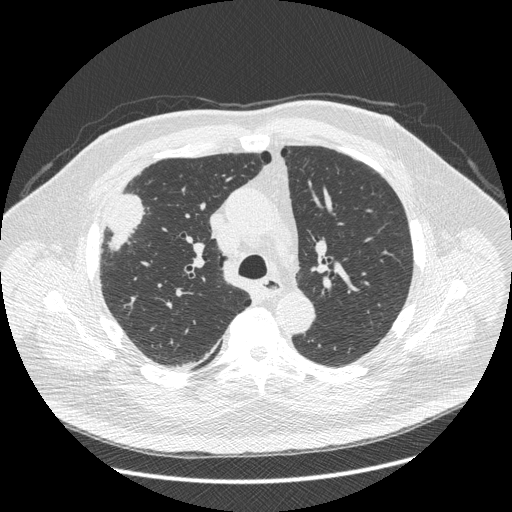
Axial slice from a low-dose chest CT screening exam; third annual screen; lung window (W 1500 / L -600 HU); 1.25 mm slice thickness; standard (soft-tissue) reconstruction kernel (STANDARD); slice 139 of 426 in the series. Male, age 66 years at enrolment. Current smoker at enrolment.
Expert reader's lesion annotation, bounding box (x1, y1, x2, y2) in pixels: (87, 190, 146, 266). Screening reader's record for this exam (one nodule recorded; not confirmed to be the boxed lesion): non-calcified nodule or mass ≥4 mm, right upper lobe, 48 × 25 mm, spiculated (stellate) margins, soft tissue attenuation, pre-existing on the prior screen: no. Lung cancer was diagnosed 35 days after this screen: non-small cell carcinoma, right upper lobe, stage IV (AJCC 6th edition), 50 mm at pathology.